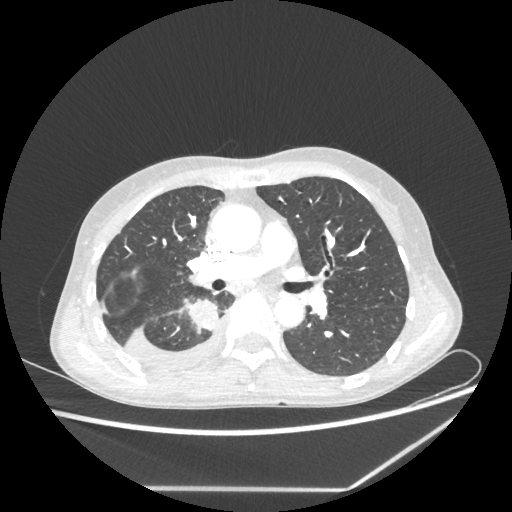
Chest CT, one axial slice. Slice 135 of 237 in the series (ordered by position). Reconstruction kernel STANDARD. 80 kVp. Lung window (W 1500 / L -600 HU). 1.25 mm slice thickness. 512 × 512 image matrix. Patient: female, 59 years. Case-level facts recorded for this patient, not image findings: clinical TNM (as recorded): T1c N1 M1.
Structures marked on this image (rectangle marked by the reading radiologist):
- lung tumour (recorded histology: adenocarcinoma): bounding box (x1, y1, x2, y2) in pixels: (185, 297, 222, 333)